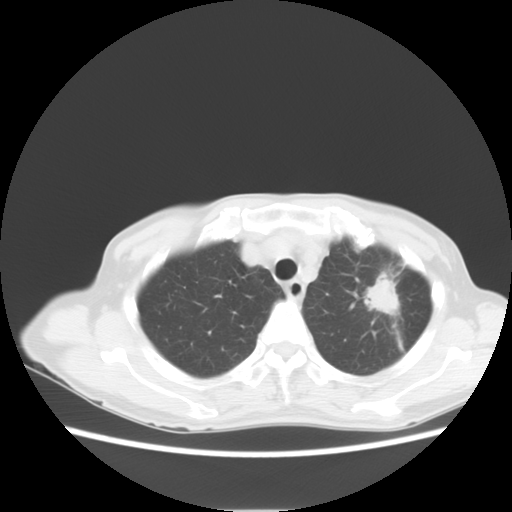
Chest CT, one axial slice; slice 10 of 14 in the series (ordered by position); 120 kVp; lung window (W 1500 / L -600 HU); 5 mm slice thickness; 512 × 512 image matrix, field of view 350 × 350 mm. Female patient, age 71 years. From the clinical record (not read from this slice): clinical TNM (as recorded): T2 N0 M0.
Structures marked on this image (bounding box drawn by a radiologist):
- lung tumour (recorded histology: adenocarcinoma): box from (x=360, y=274) to (x=403, y=318) px